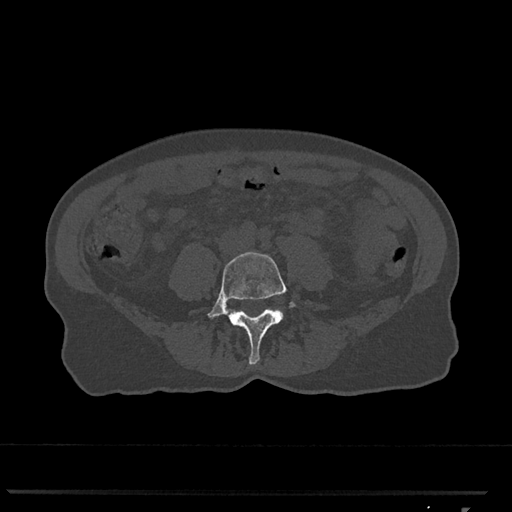
CT including the spine, one axial slice. Slice 205 of 793 in the series (ordered by position). Reconstruction kernel Br40s/3. Bone window (W 1800 / L 400 HU). 0.5 mm slice thickness. 512 × 512 image matrix. Female patient, age 62 years. From the clinical record (not read from this slice): primary cancer: renal.
Outlined on this slice (semi-automatically segmented with operator editing):
- L4 vertebra: bounding box [x1, y1, x2, y2] px = [207, 252, 296, 365]